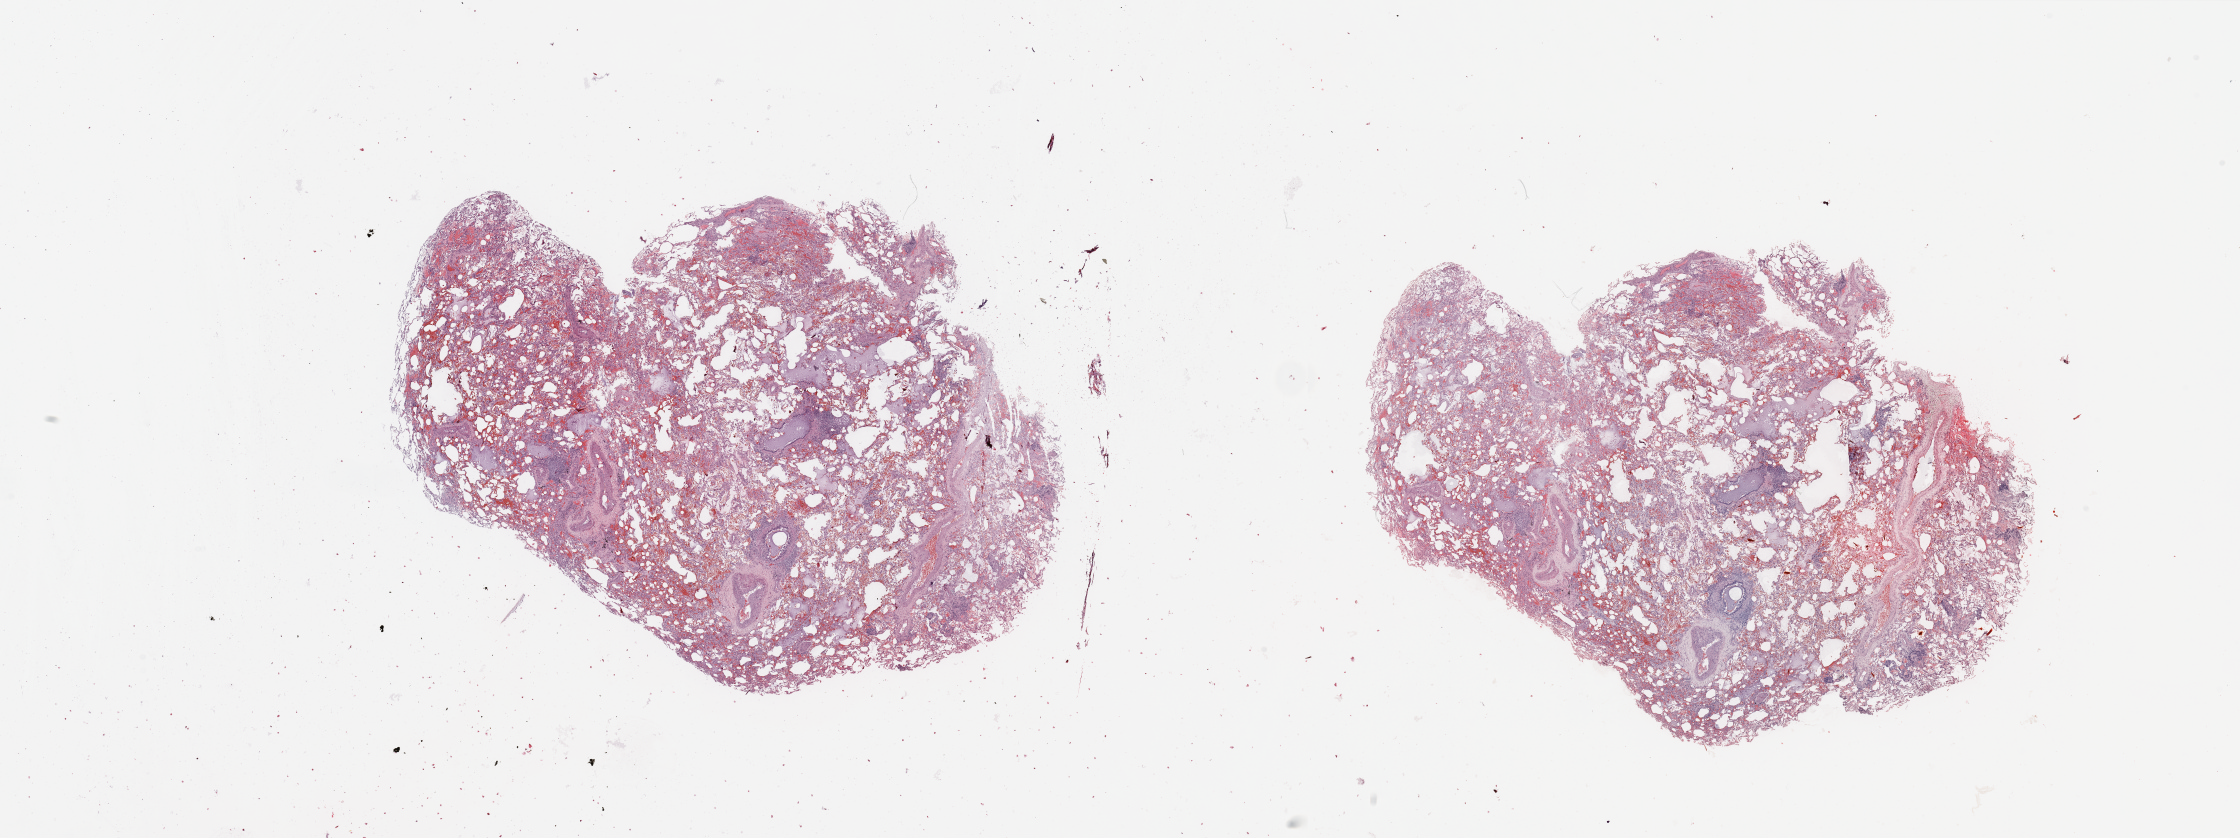
H&E whole-slide image, shown as a low-resolution overview of the whole scanned area (about 35.4 x 13.3 mm), normal (non-tumour) tissue sample, sampled site: lung. Male, 39 y/o.
• this section: normal (non-tumour) tissue from the same patient
• patient diagnosis: Adenocarcinoma, NOS